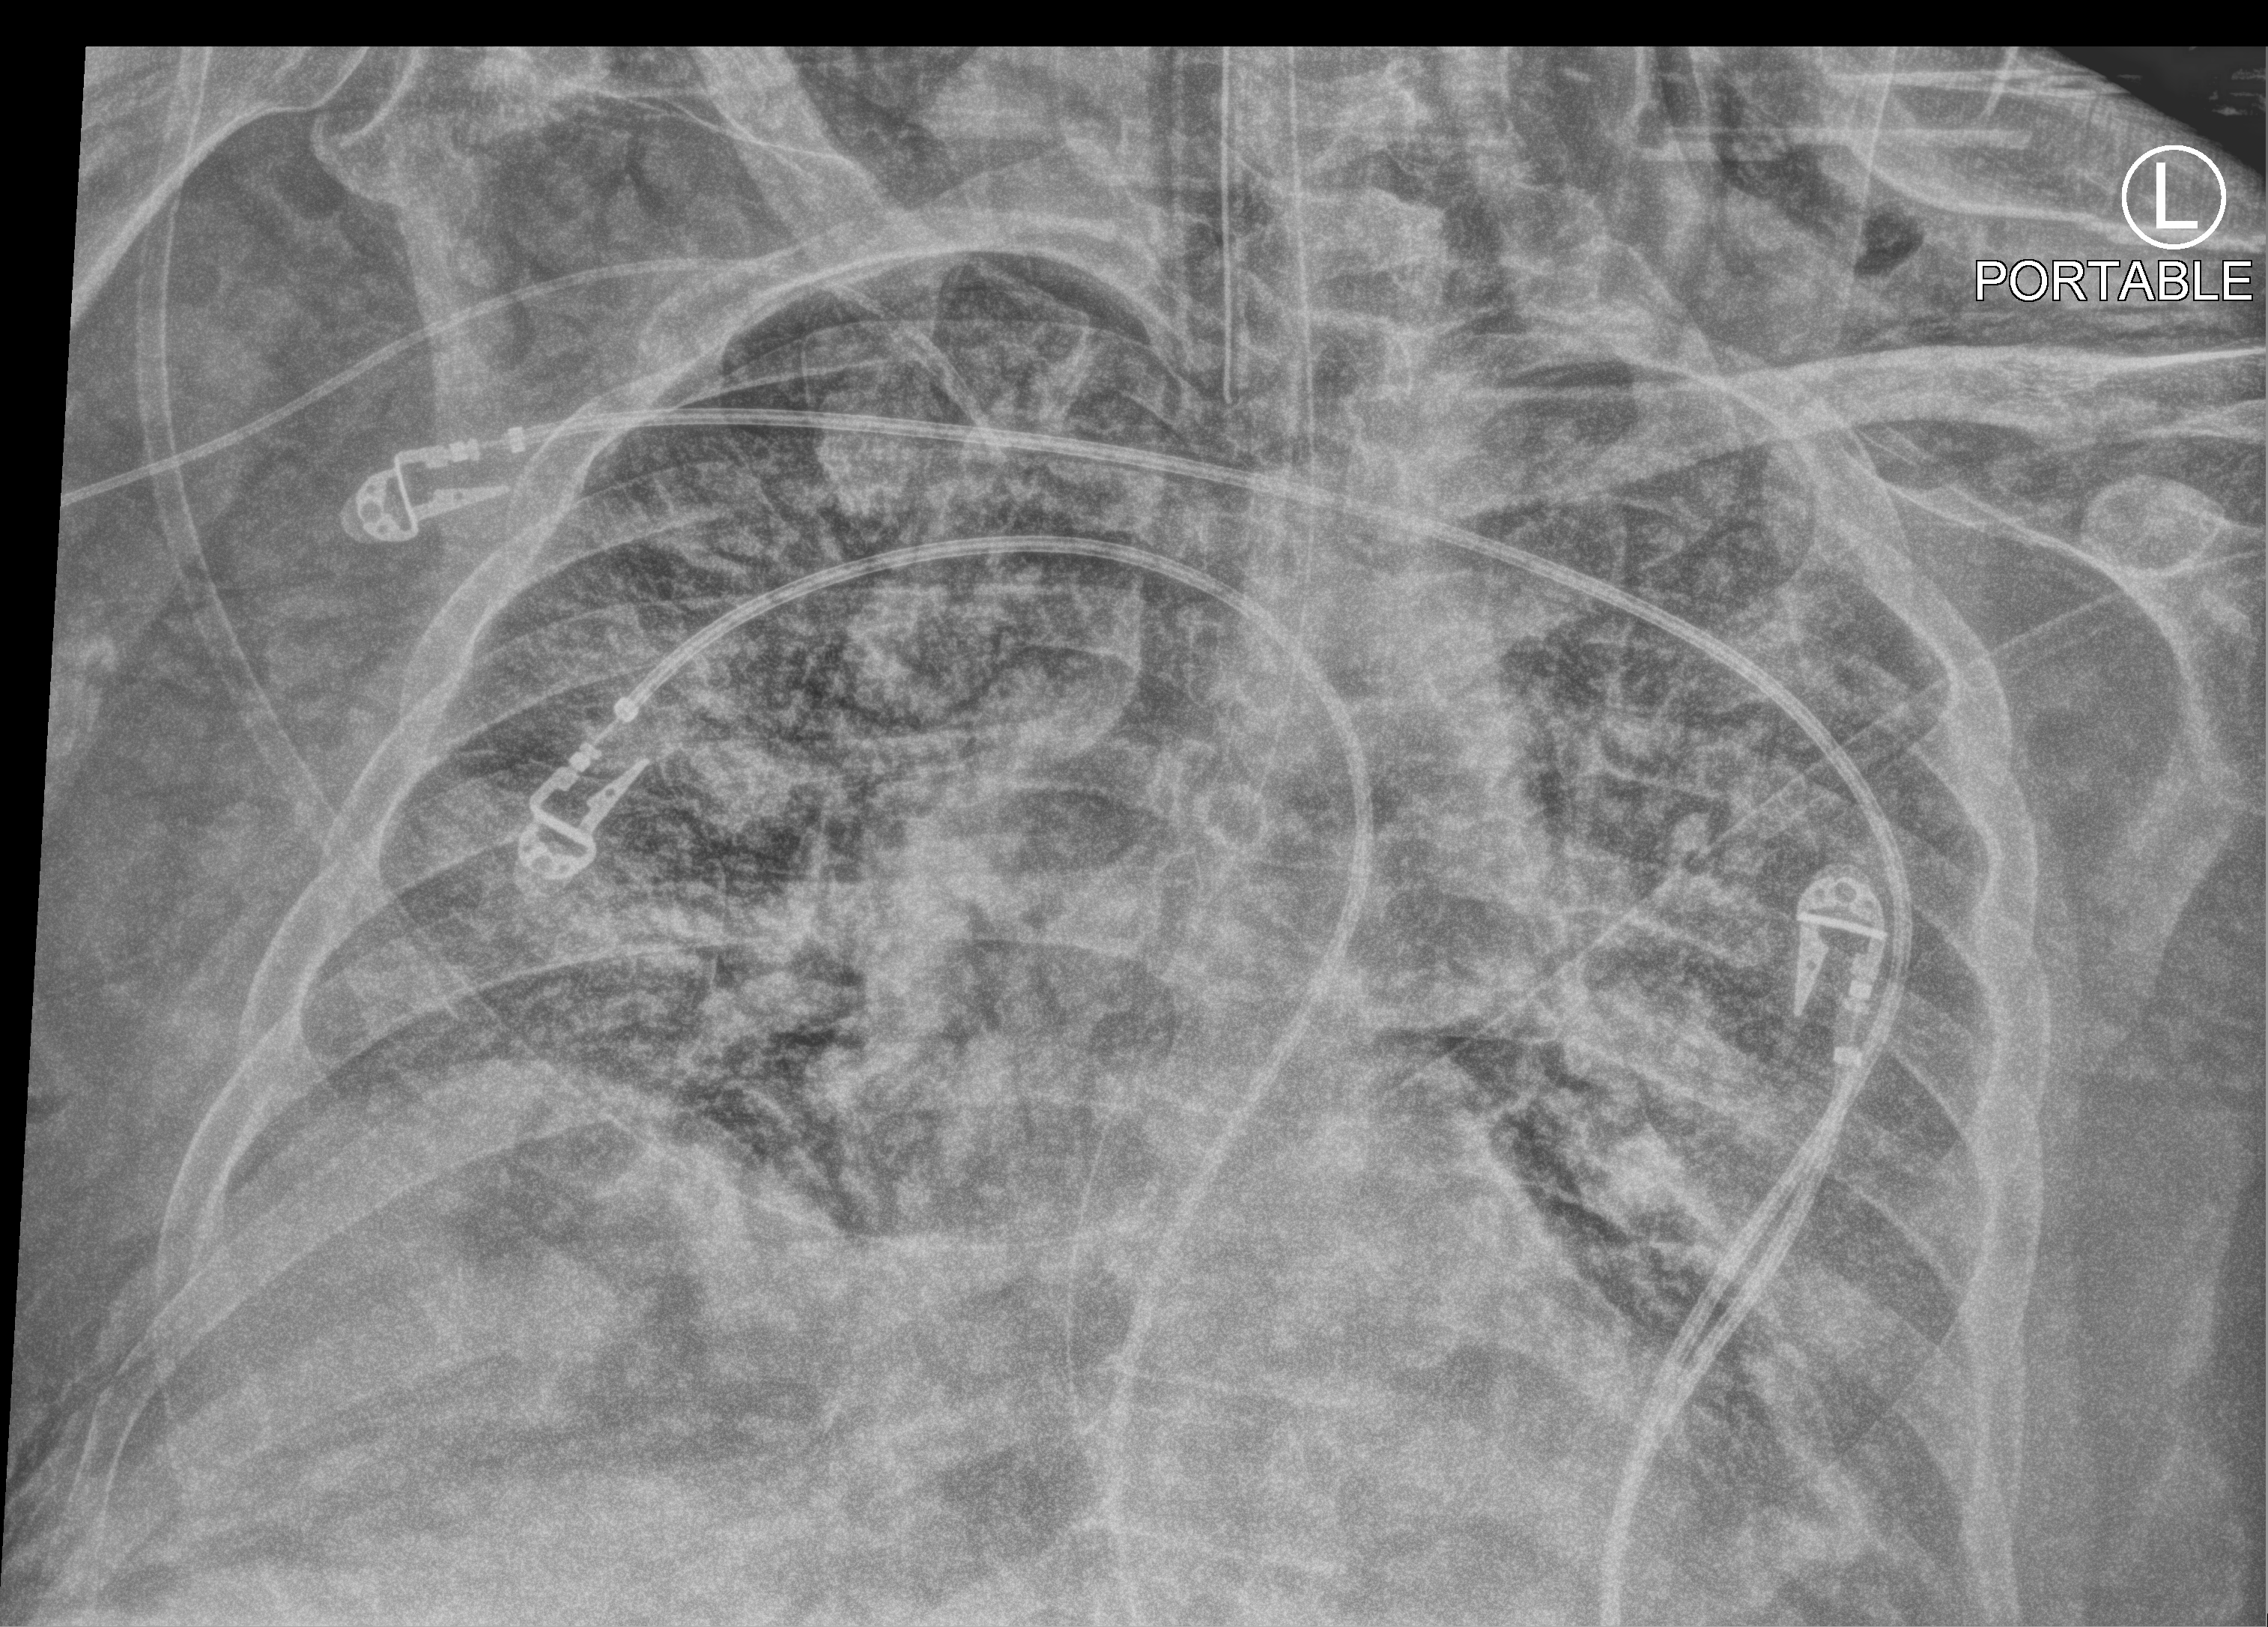
Portable chest radiograph; anteroposterior (AP) projection. Adult patient hospitalised with COVID-19, age 18–59 years.
From the hospital-stay record, not from the radiograph (when in the stay this image was taken is not recorded): admitted to intensive care during this hospital stay: yes; hypertension (admission record): yes.